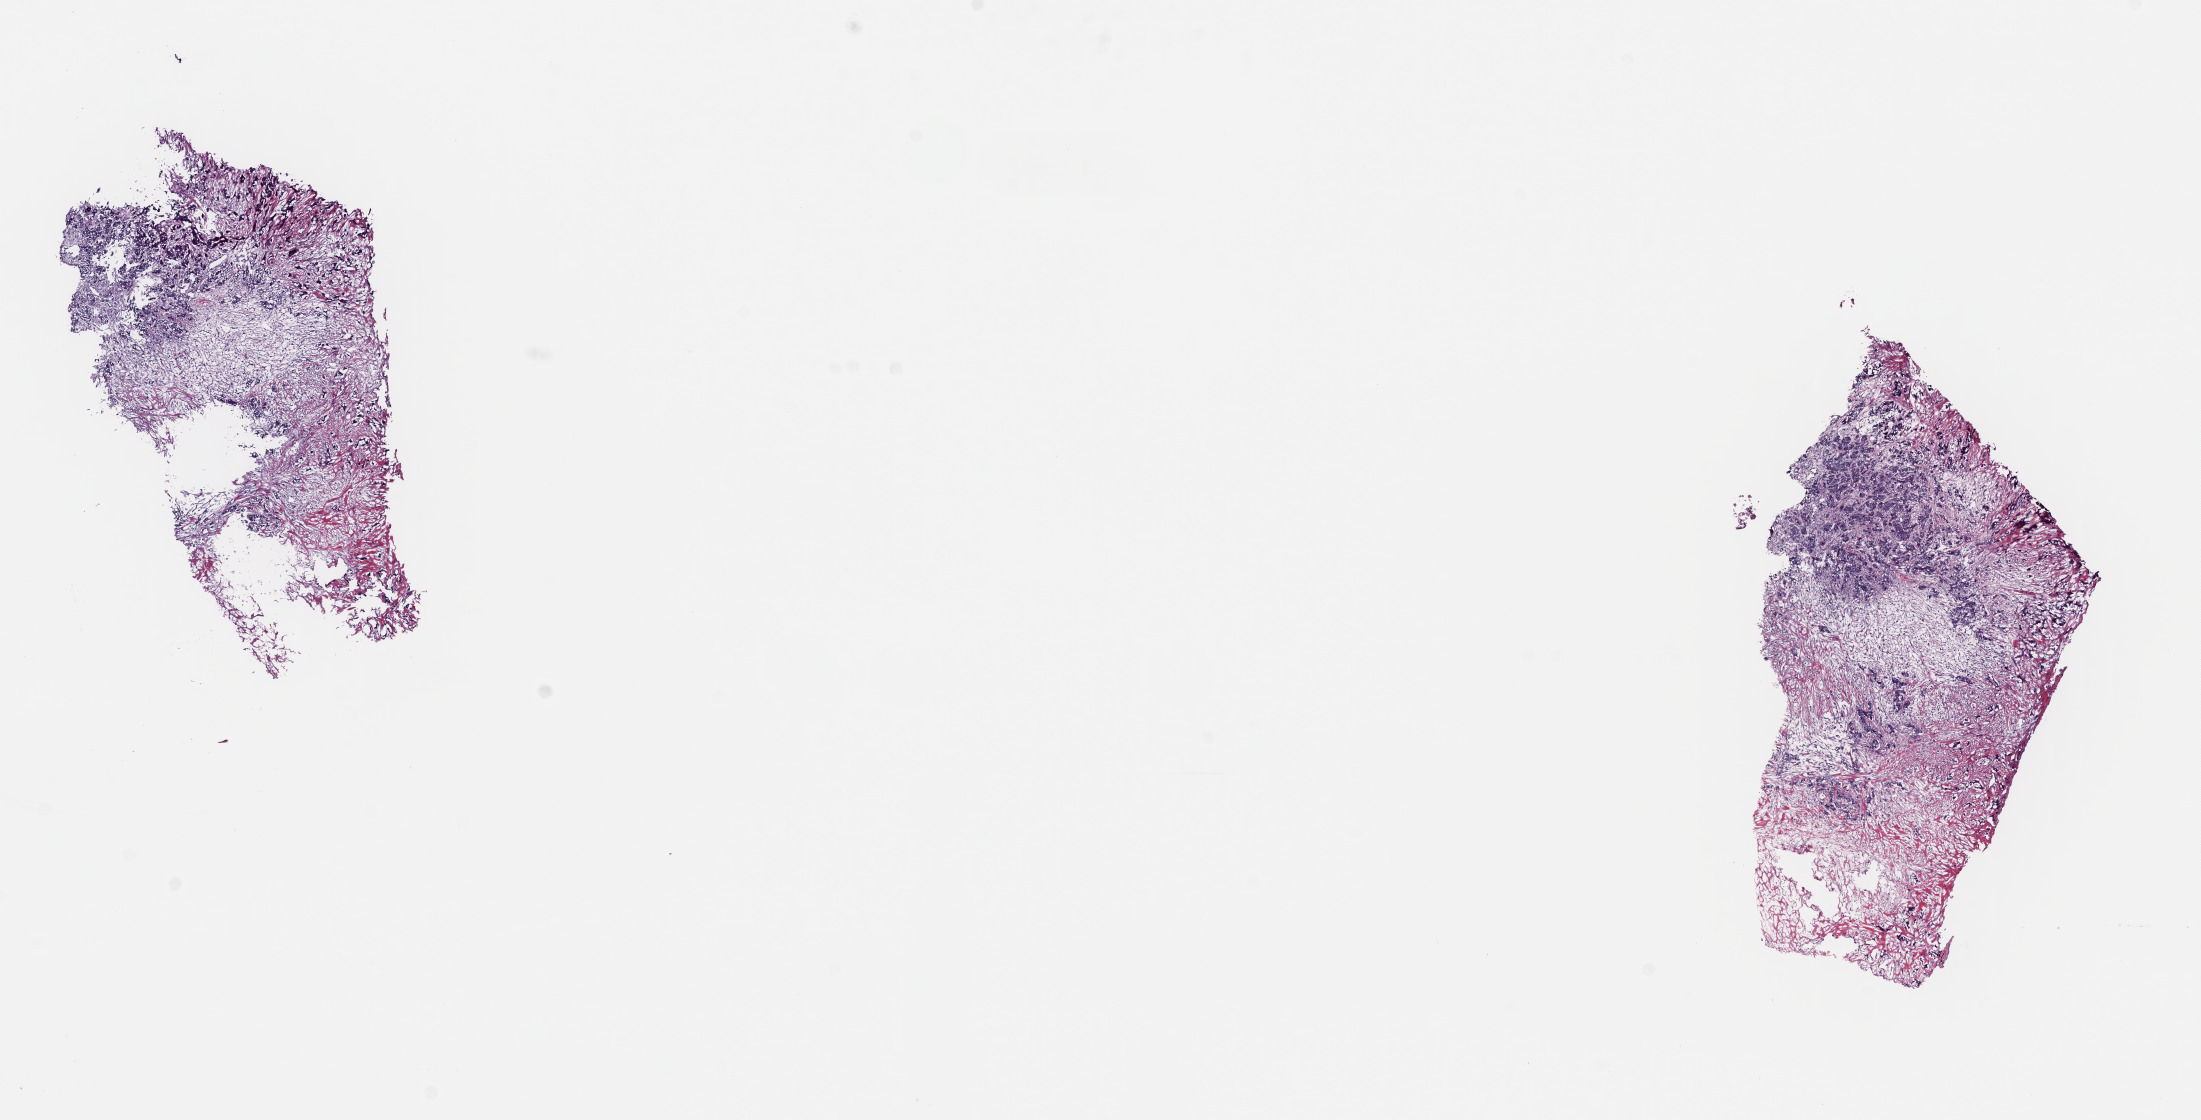
Whole-slide histology image, Hematoxylin and eosin (H&E) stained — shown as a low-resolution overview of the whole scanned area (about 17.4 x 8.8 mm, from a 40x scan), frozen section, primary tumour sample from the breast. Patient: female, age at initial diagnosis 54 years. Slide review estimates, as recorded: tumour cells 40%, tumour nuclei 60%, normal cells 0%, stromal cells 60%, necrosis 0%. Inflammatory infiltration, as recorded: lymphocyte infiltration 0%, monocyte infiltration 0%, neutrophil infiltration 0%.
AJCC pathologic stage: IIA (7th edition). TNM: T2 N0 M0. Lymph nodes positive (case pathology): 0 of 1 examined. Pathologic diagnosis: Infiltrating duct carcinoma, NOS.